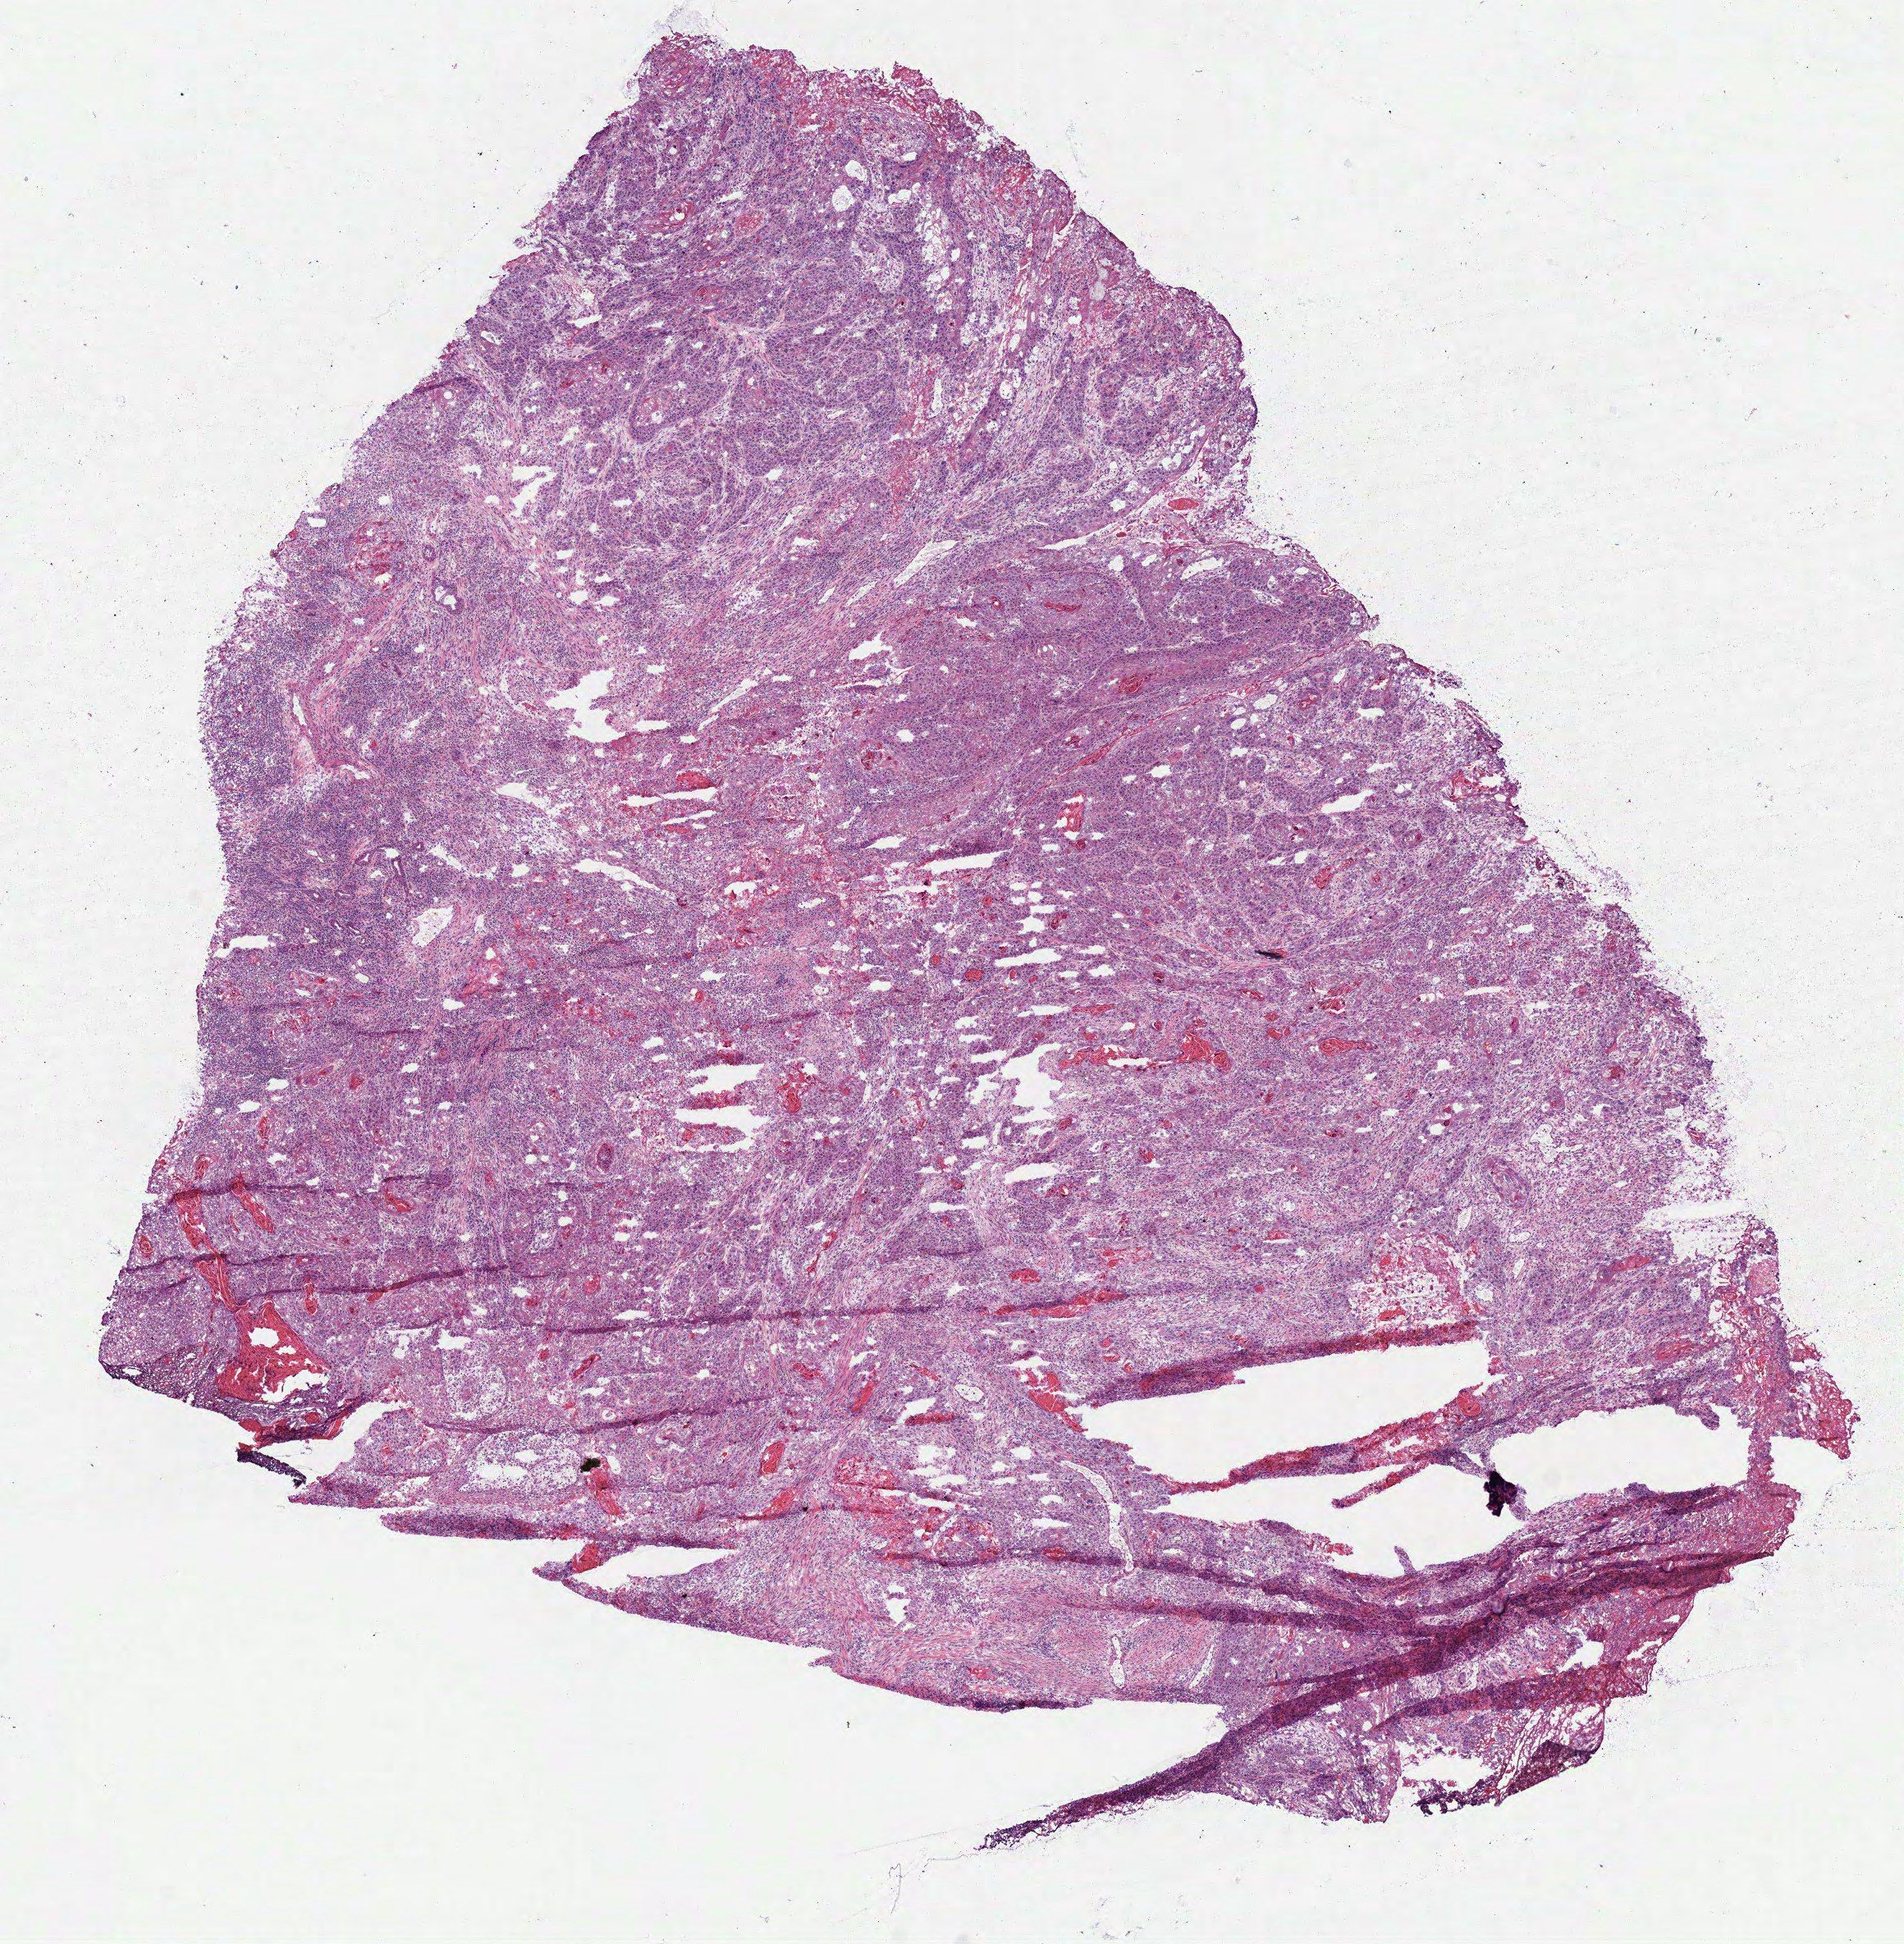
H&E-stained whole-slide image — low-resolution overview of the scanned area, about 9.1 x 9.3 mm (acquisition: 40x scan), frozen section, primary tumour sample from the head and neck. Male patient; age at initial diagnosis 47 years. Histologic grade: G2 (moderately differentiated). Pathologist review of this section (percent, as recorded): tumour cells 97%, tumour nuclei 75%, necrosis 3%. Inflammatory infiltration, as recorded: lymphocyte infiltration 15%, neutrophil infiltration 5%.
* laterality: midline
* AJCC pathologic stage: IVA (6th edition)
* histologic diagnosis: Squamous cell carcinoma, NOS (floor of mouth, NOS)